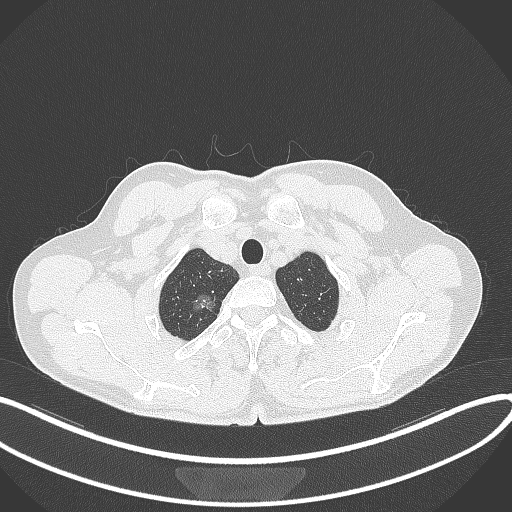
Chest CT, one axial slice. Slice 348 of 407 in the series (ordered by position). 120 kVp. Lung window (W 1500 / L -600 HU). 1 mm slice thickness. 512 × 512 image matrix, field of view 400 × 400 mm. Male patient, age 58 years. Case-level facts recorded for this patient, not image findings: clinical TNM (as recorded): T1c N0 M0; histopathological grade: G1-2.
Structures marked on this image (rectangle marked by the reading radiologist):
- lung tumour (recorded histology: adenocarcinoma): bounding box [x1, y1, x2, y2] px = [192, 289, 220, 318]